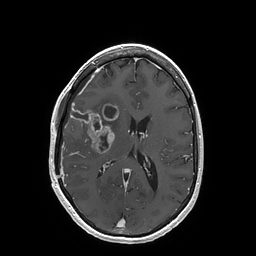
Brain MRI from a brain-tumour surgery series, one axial slice. Slice 75 of 202 in the series (ordered by position). T1-weighted post-contrast. 1 mm slice thickness. 256 × 256 image matrix, field of view 250 × 250 mm. From the clinical record (not read from this slice): histopathology: Glioblastoma; WHO grade: 4; IDH mutation: no; tumour location: Right Insular.
Annotated regions visible in this slice (manually delineated by an expert):
- tumour: box from (x=69, y=104) to (x=118, y=153) px